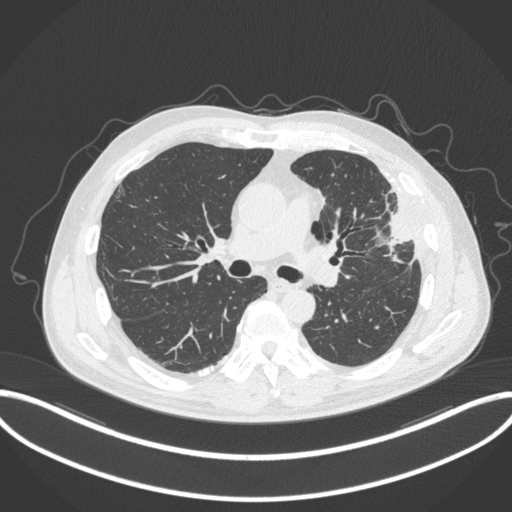
Chest CT, one axial slice; slice 200 of 382 in the series (ordered by position); 120 kVp; lung window (W 1500 / L -600 HU); 1 mm slice thickness; 512 × 512 image matrix, field of view 415 × 415 mm. Male patient, age 64 years. Case-level facts recorded for this patient, not image findings: clinical TNM (as recorded): T4 N1 M0; histopathological grade: G3.
Outlined on this slice (rectangle marked by the reading radiologist):
- lung tumour (recorded histology: adenocarcinoma): bounding box [x1, y1, x2, y2] px = [376, 190, 421, 261]